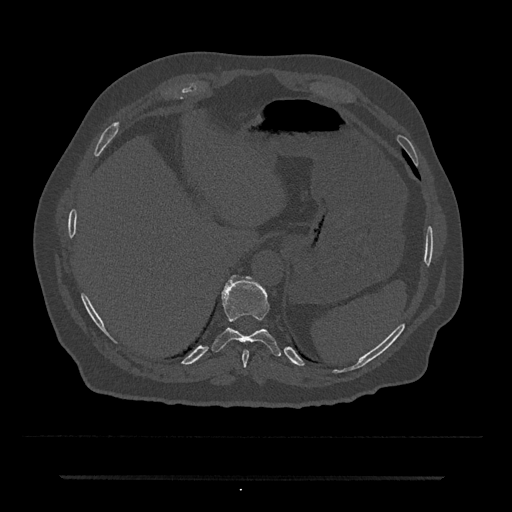
CT including the spine, one axial slice; position 233 of 797 along the scan axis; reconstruction kernel Br40s/3; 120 kVp; bone window (W 1800 / L 400 HU); 0.5 mm slice thickness; 512 × 512 image matrix. Patient: male, 69 years. Case-level facts recorded for this patient, not image findings: primary cancer: prostate.
Annotated regions visible in this slice (semi-automatic segmentation, software-assisted and operator-edited):
- T10 vertebra: box from (x=212, y=275) to (x=281, y=356) px
- T11 vertebra: (x=230, y=276)–(x=235, y=280)
- T9 vertebra: (x=242, y=349)–(x=249, y=367)